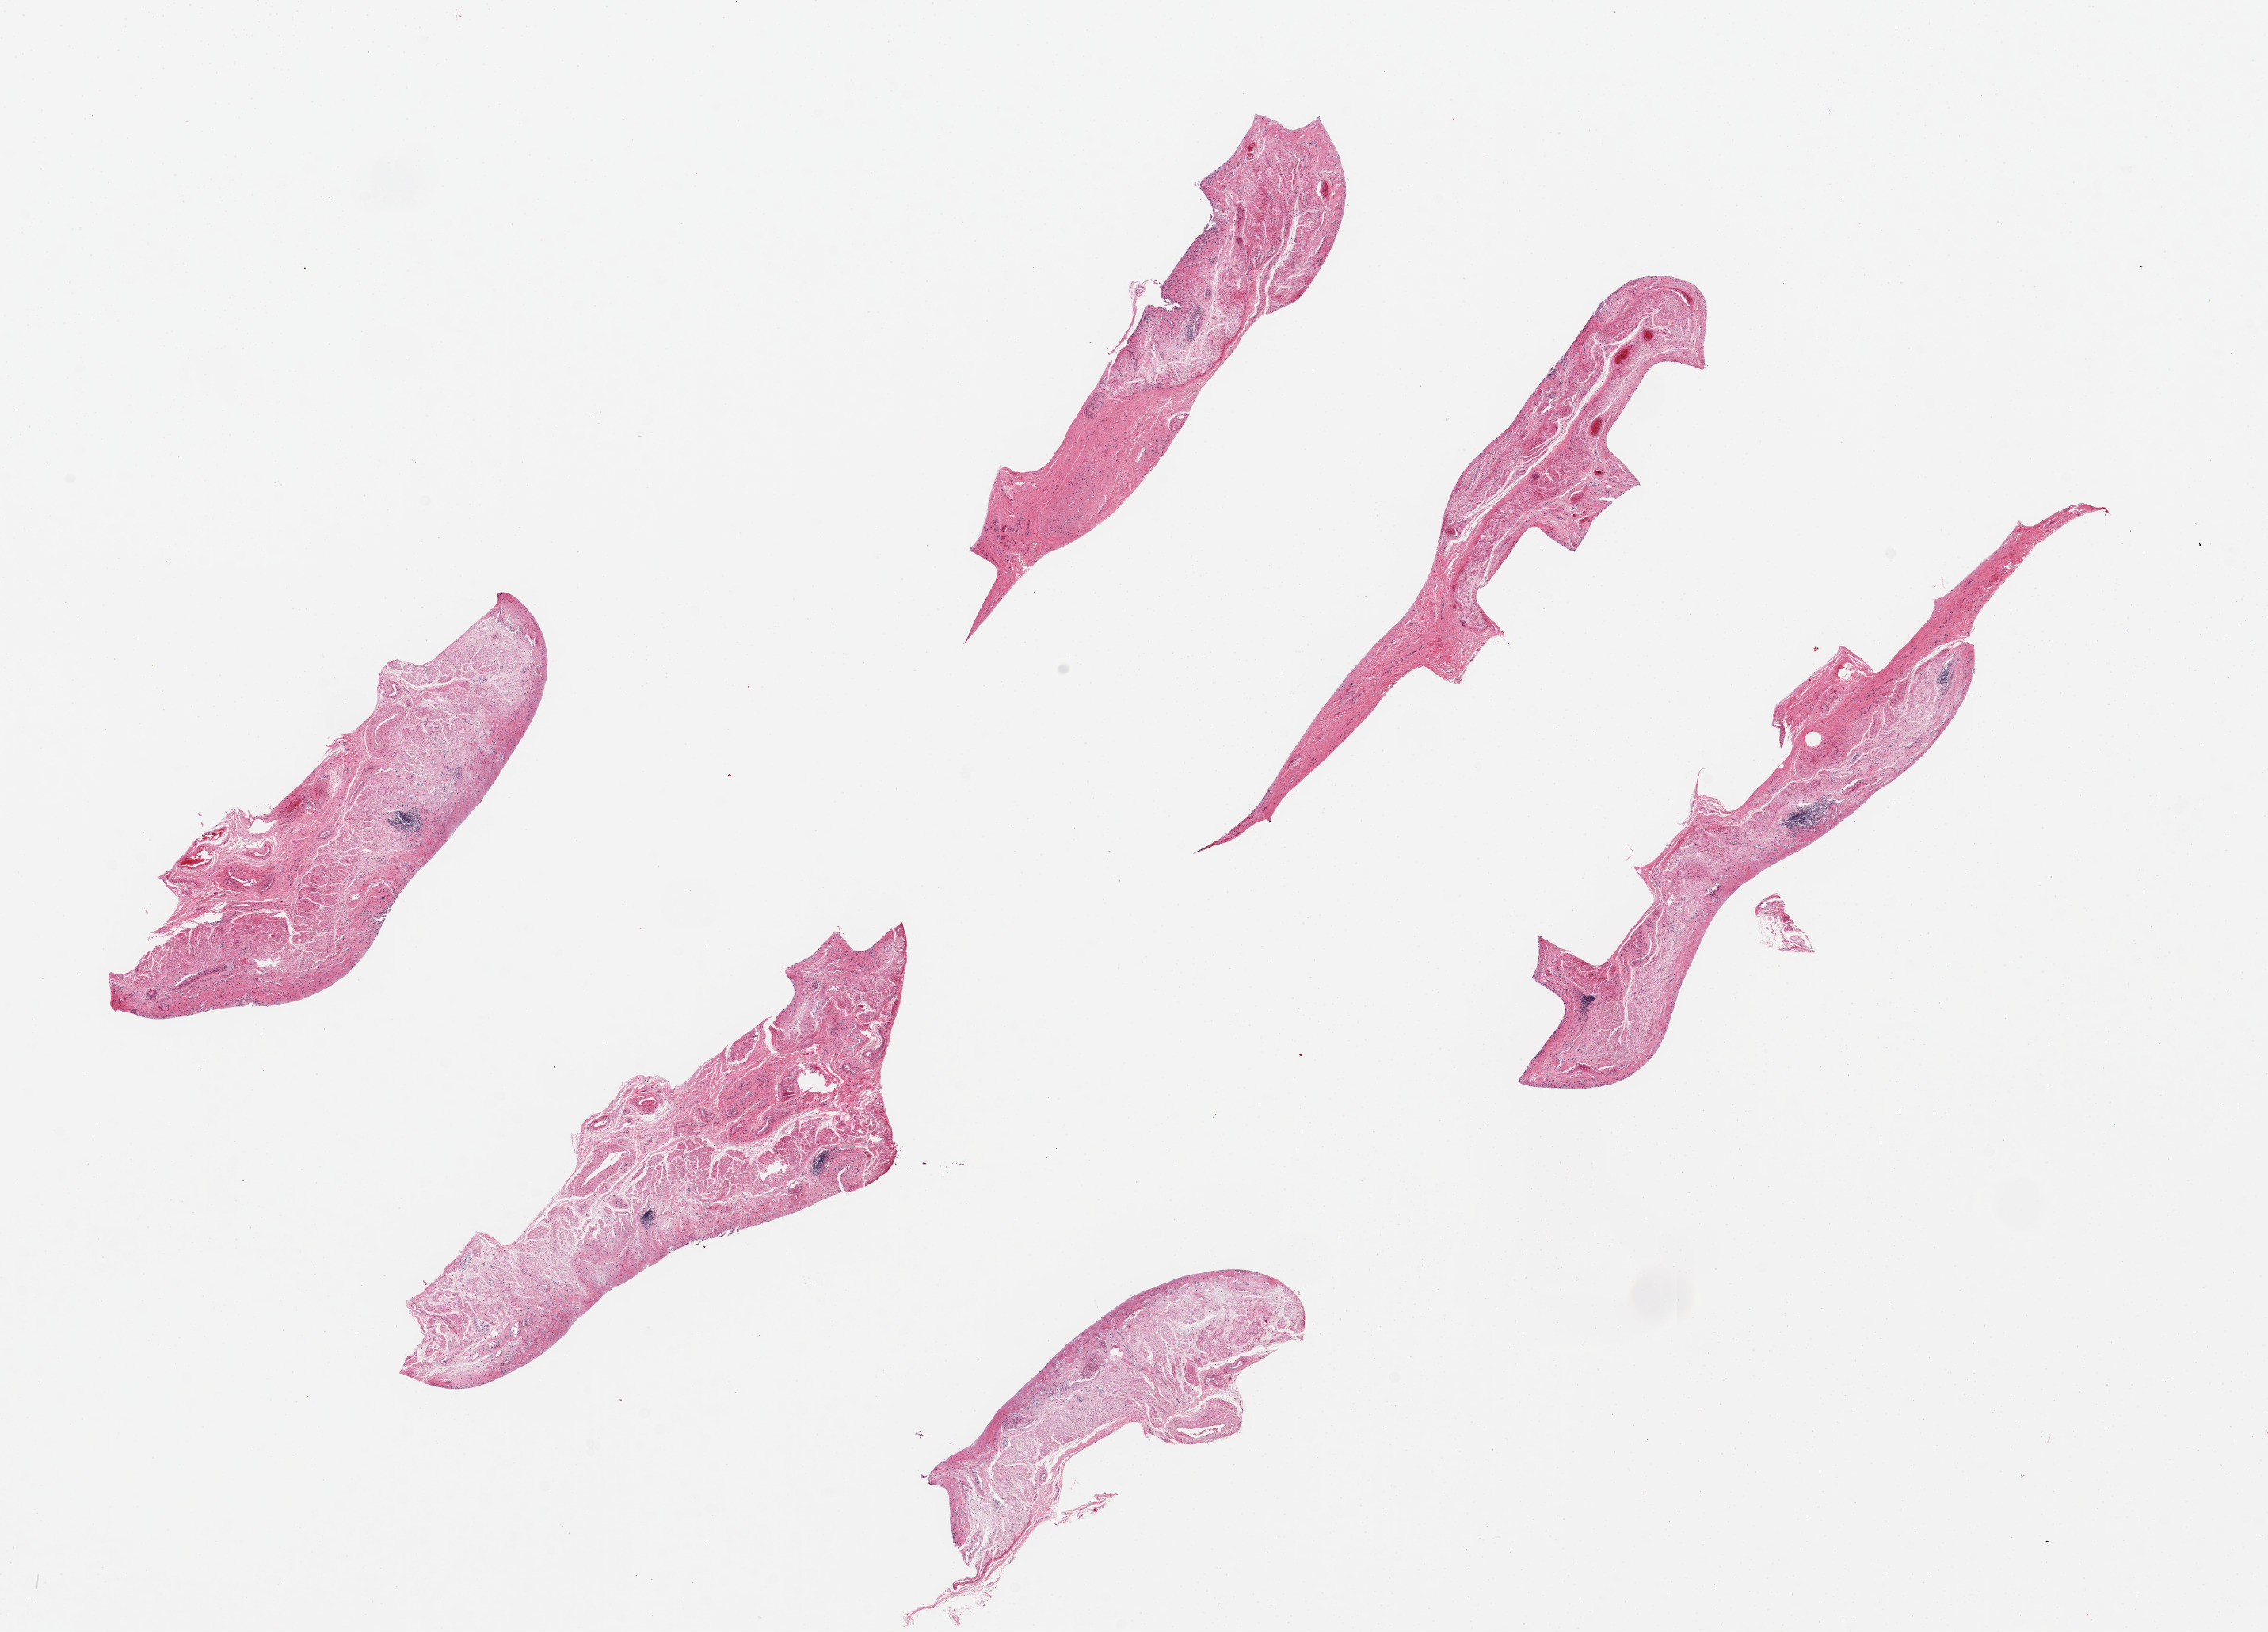
H&E whole-slide image, brightfield — low-resolution overview of the scanned area, about 22.6 x 16.3 mm (from a 20x scan); PAXgene-fixed, paraffin-embedded tissue; section of esophageal mucous membrane (target tissue); donor tissue sample. Donor sex: male.
Pathologist's review note for this sample: 6 pieces up to 8x2 mm; mucosa totally sloughed; only submucosa and muscularis mucosa remain.